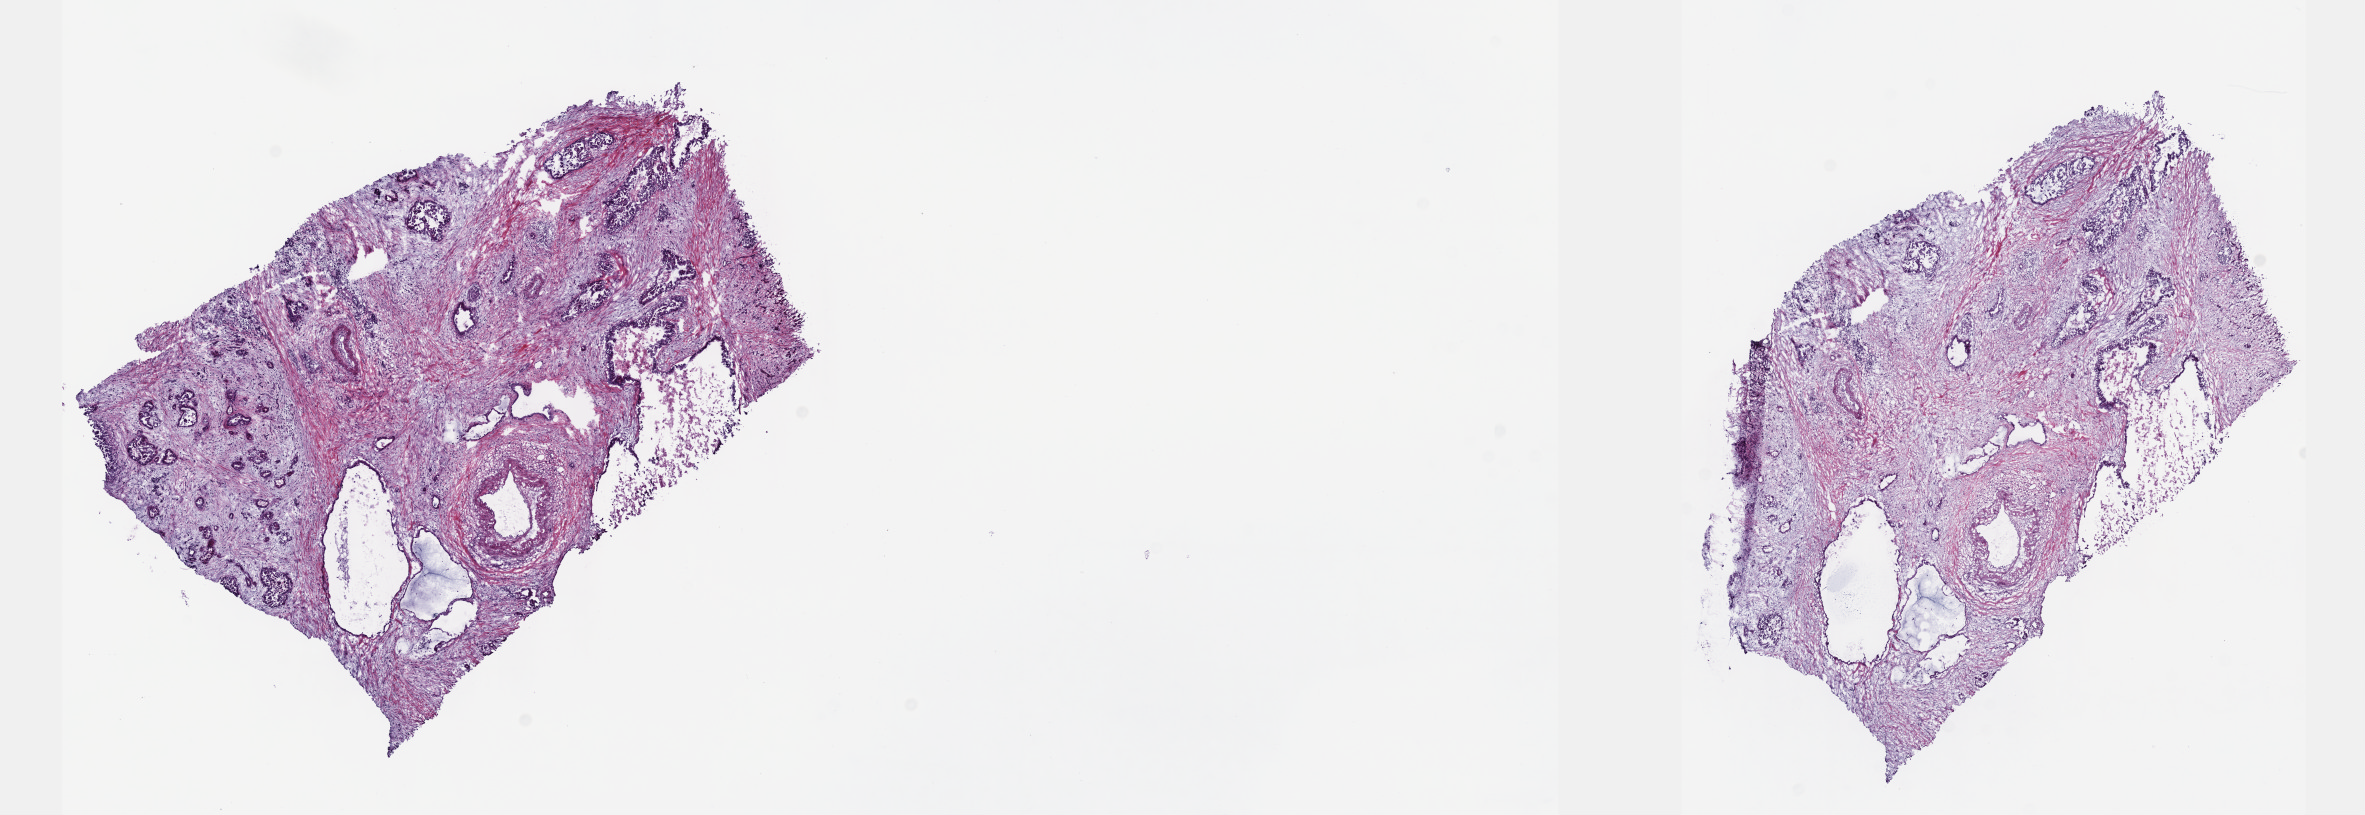
Whole-slide histology image, H&E, low-resolution overview of the scanned area, about 19.1 x 6.6 mm (slide scanned at 40x), frozen section, primary tumour sample from the pancreas. Female patient; age at initial diagnosis 66 years. Histologic grade: G2 (moderately differentiated). Composition of this section per pathologist review: tumour cells 50%, tumour nuclei 50%, normal cells 10%, stromal cells 40%, necrosis 0%. Infiltration values recorded for this section: lymphocyte infiltration 40%, monocyte infiltration 20%, neutrophil infiltration 20%.
• lymph nodes positive (case pathology): 0 of 8 examined
• histologic diagnosis: Infiltrating duct carcinoma, NOS (body of pancreas)
• AJCC pathologic stage: IA (7th edition)